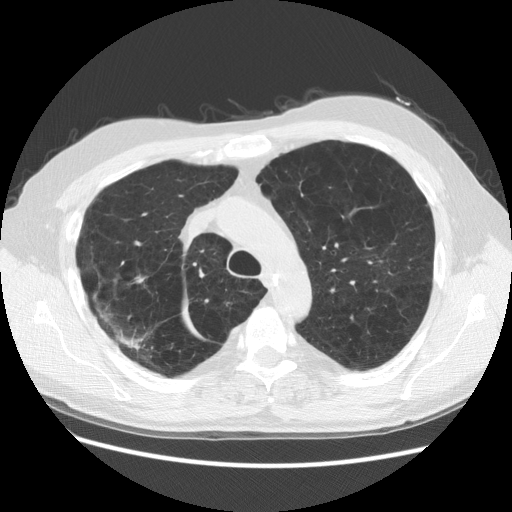
Low-dose screening chest CT, one axial slice. Slice 101 of 137 in the series (ordered by position). Reconstruction kernel STANDARD. 140 kVp. Lung window (W 1500 / L -600 HU). 2.5 mm slice thickness. 512 × 512 image matrix, field of view 377 × 377 mm.
Structures marked on this image (expert manual segmentation):
- lesion 1 (tumor, upper lobe of right lung): bounding box <135,275,146,283> (left, top, right, bottom; pixels)
- lesion 2 (nodule, upper lobe of right lung): <116,333,142,350>